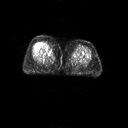
FDG PET of an extremity soft-tissue mass (from a PET/CT study), one axial slice. Slice 19 of 267 in the series (ordered by position). 3.27 mm slice thickness. 128 × 128 image matrix. Female patient, age 56 years. From the clinical record (not read from this slice): histological type: malignant solitary fibrous tumor; grade: intermediate; site of the primary tumour: right thigh.
Annotated regions visible in this slice (expert contour drawn on MRI and transferred to this co-registered scan by the dataset authors):
- gross tumour volume including surrounding oedema: bounding box <40,41,52,50> (left, top, right, bottom; pixels)